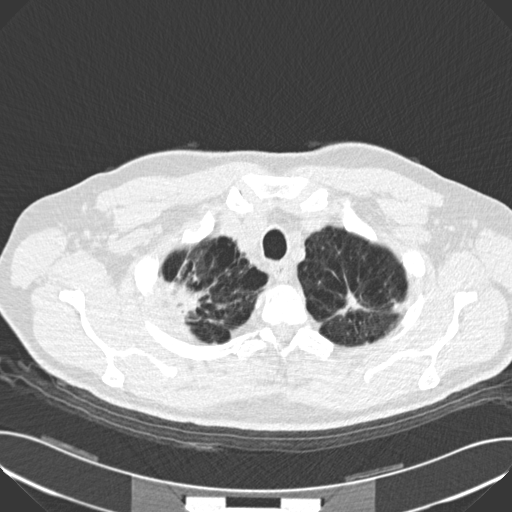
Low-dose screening chest CT, one axial slice. Slice 143 of 159 in the series (ordered by position). Lung window (W 1500 / L -600 HU). 2 mm slice thickness. 512 × 512 image matrix, field of view 380 × 380 mm.
Outlined on this slice (manually delineated by an expert):
- lesion 1 (tumor, upper lobe of right lung): bounding box [x1, y1, x2, y2] px = [167, 281, 200, 318]